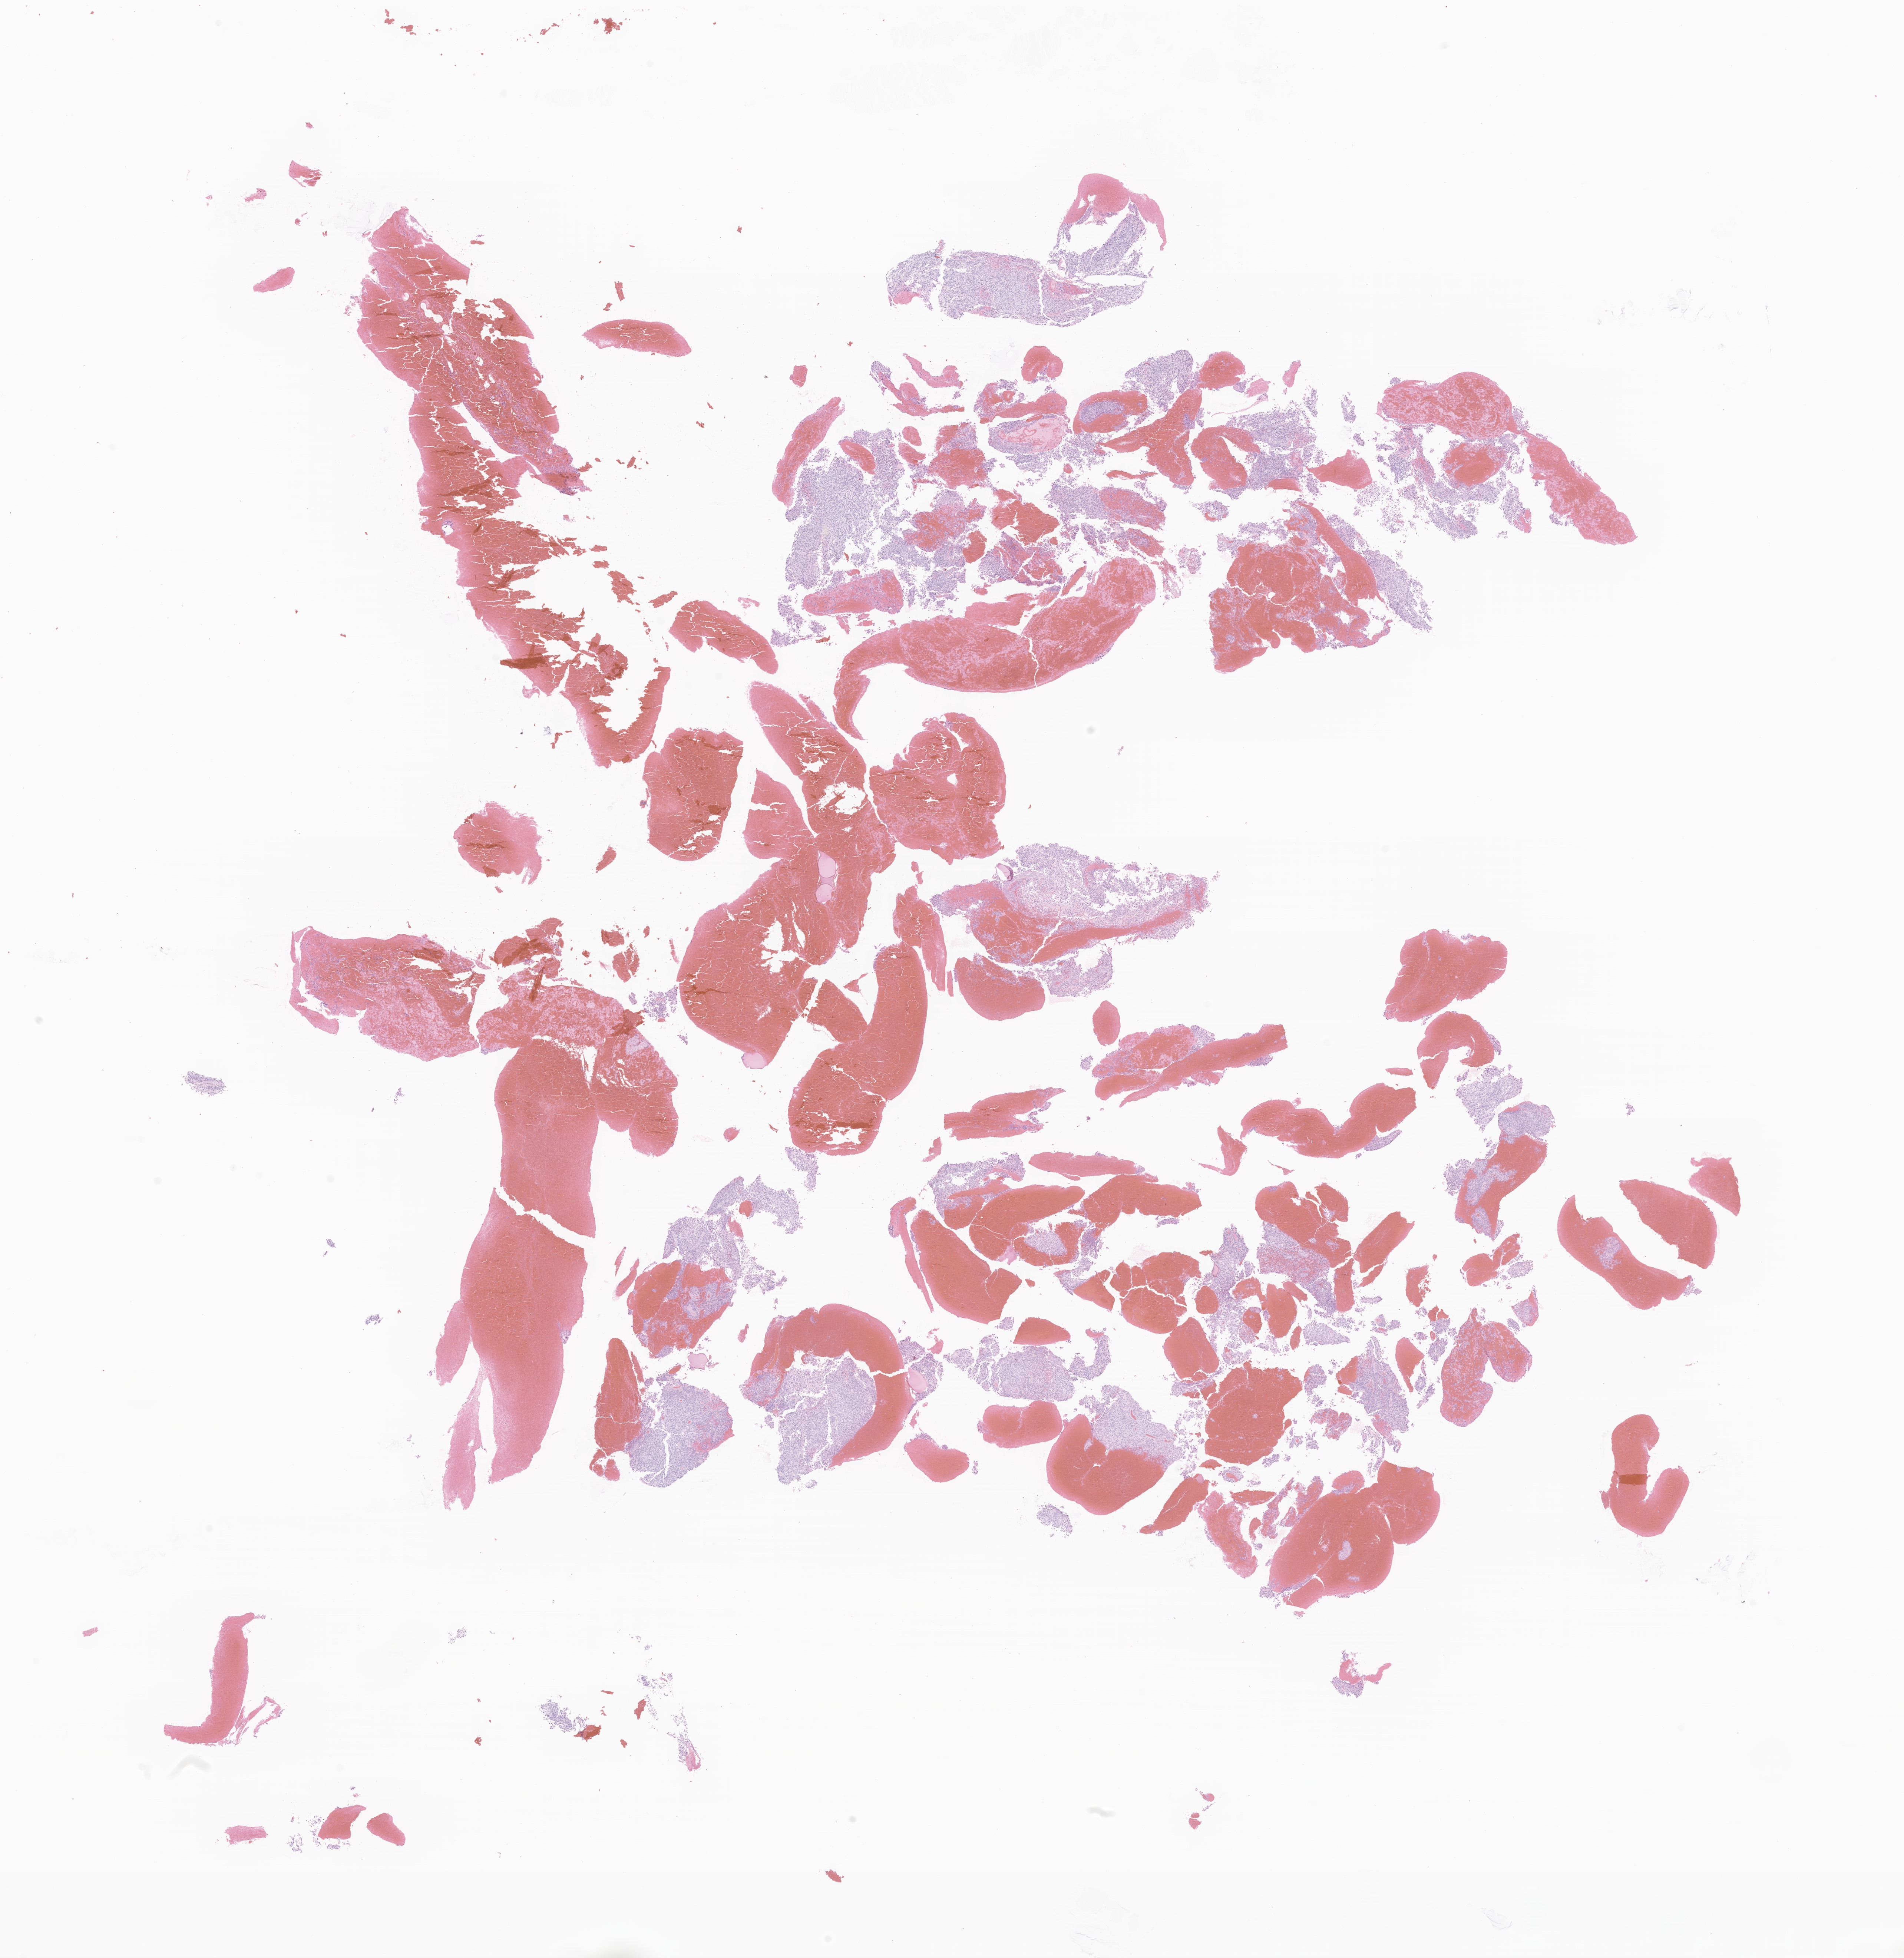
Digitized H&E-stained section of tumor tissue from the brain, whole scanned area (about 21.7 x 22.3 mm) shown as a low-resolution overview, FFPE section. Male patient, age 199 months (16 years 7 months).
Diagnosis: Glioma, malignant.